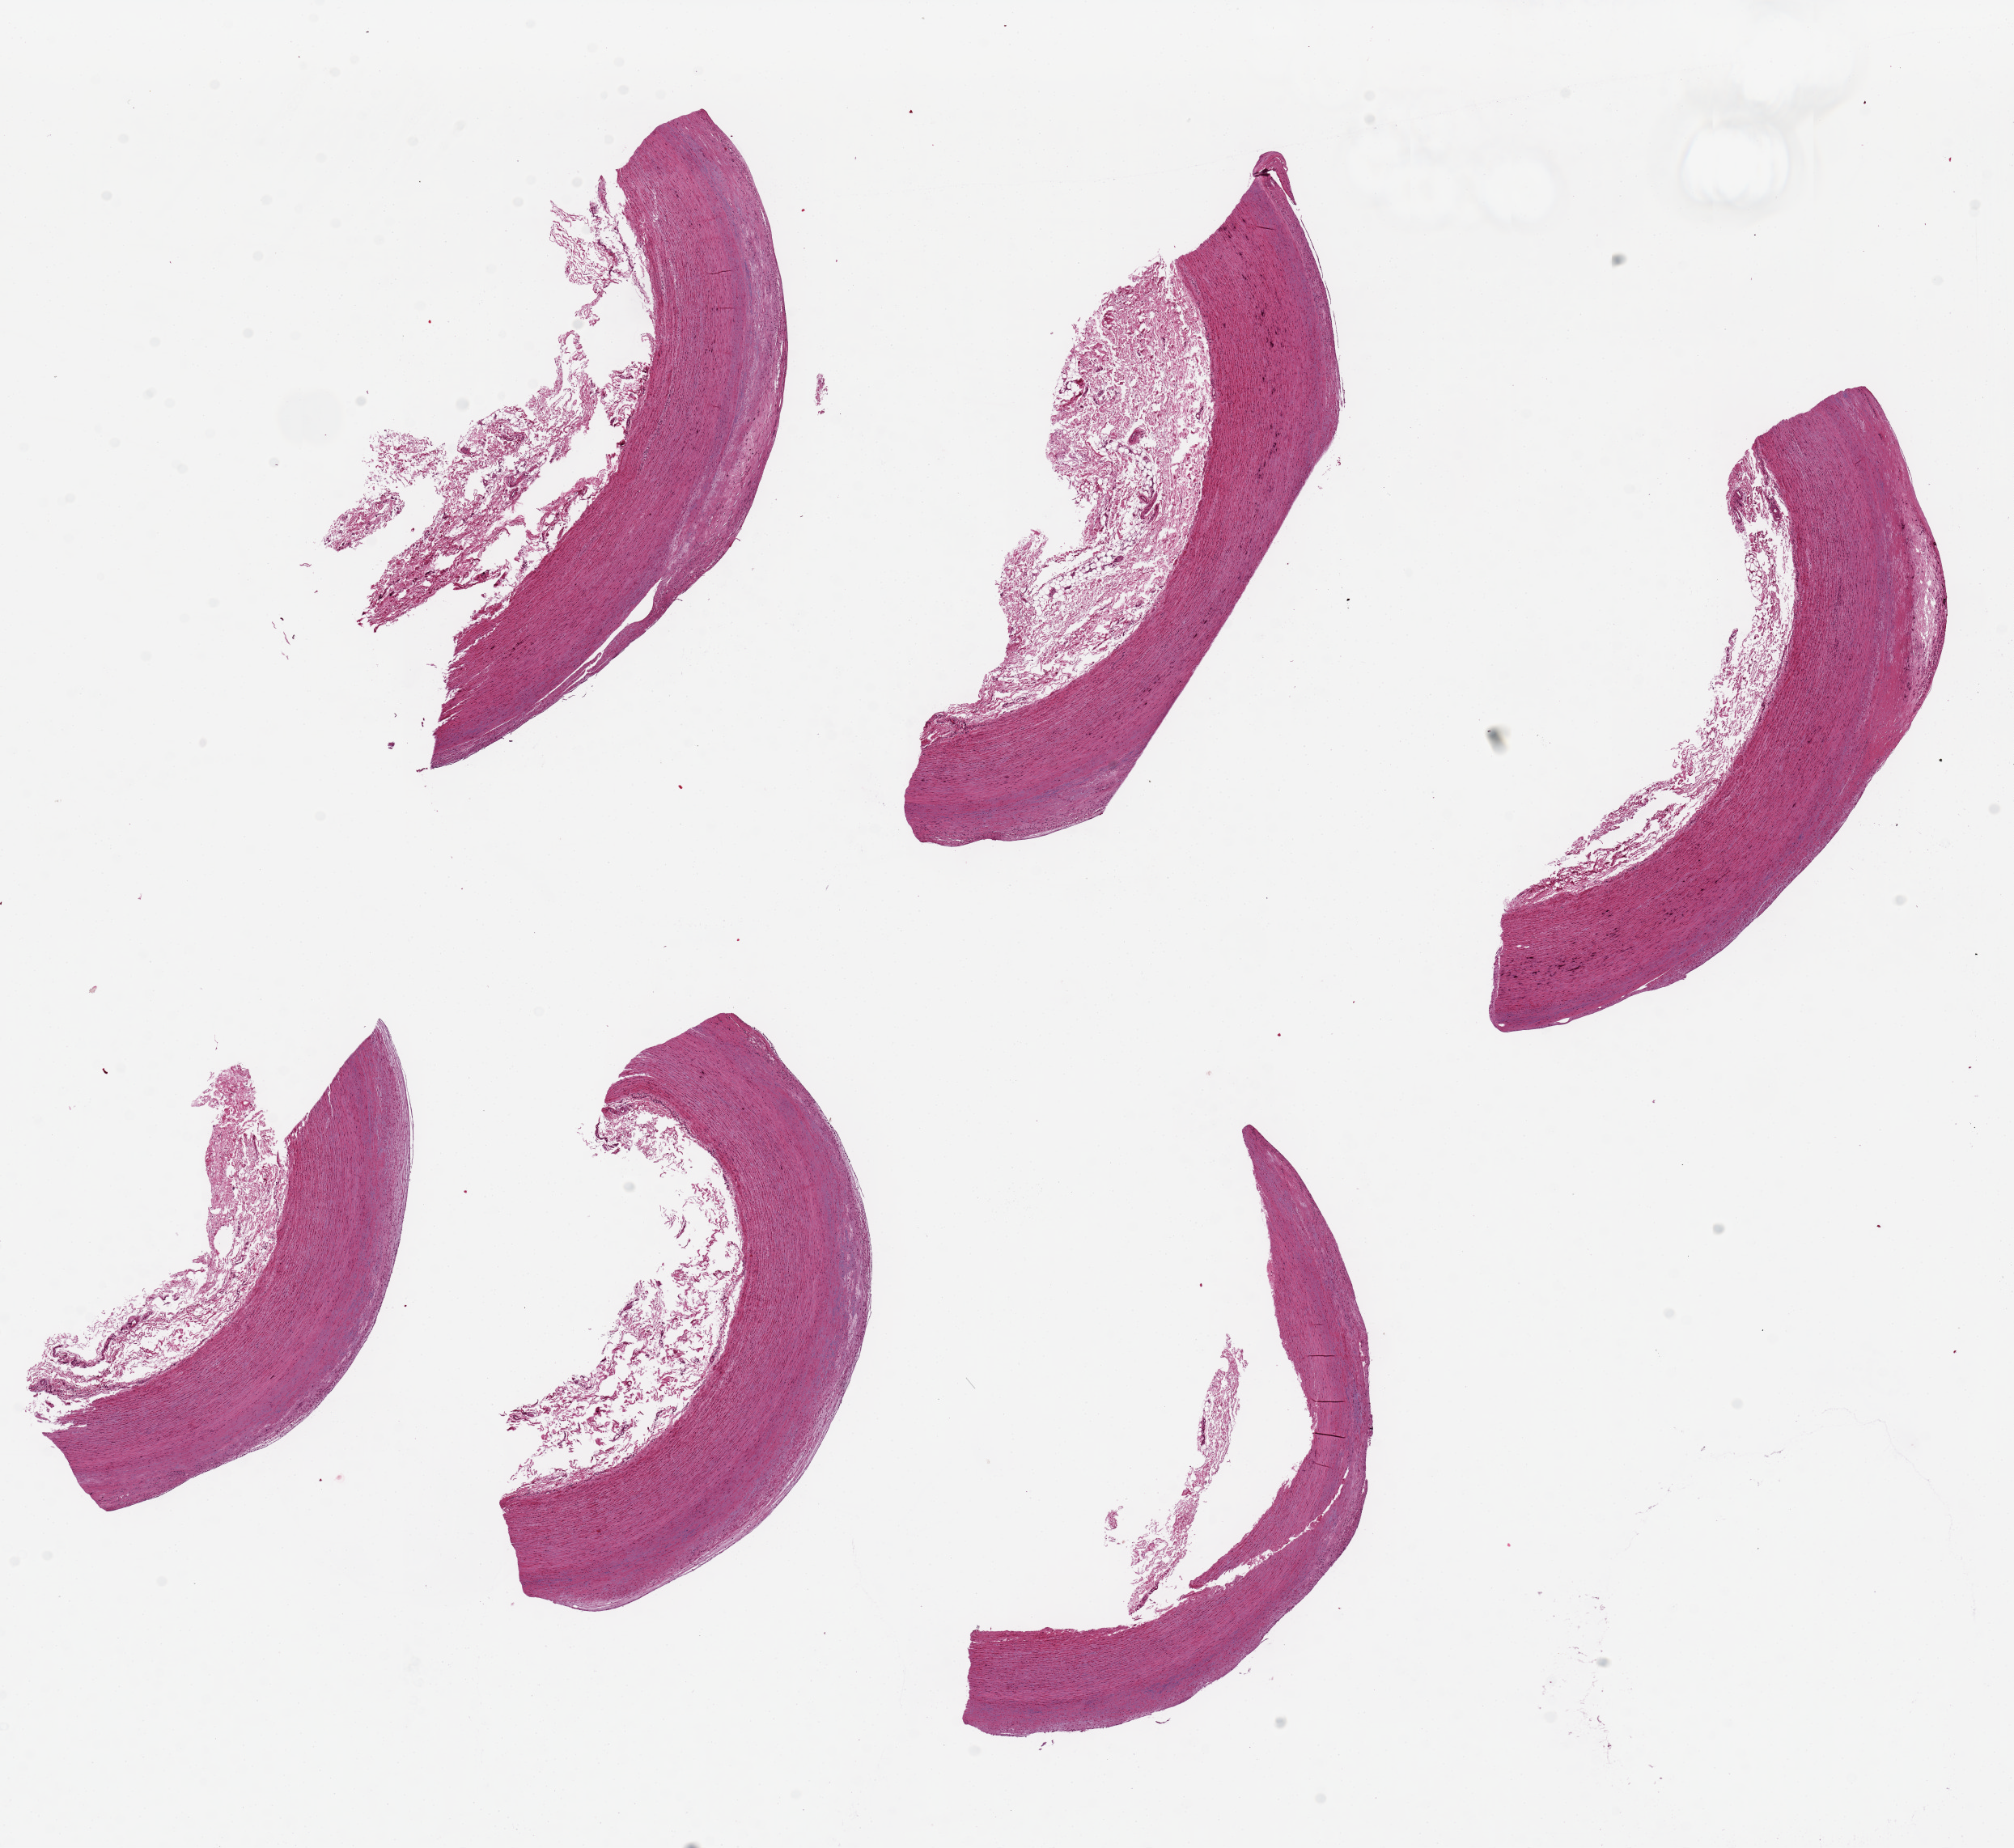
Digitized H&E-stained section — whole scanned area (about 19.7 x 18.1 mm, from a 20x scan) shown as a low-resolution overview; PAXgene-fixed, paraffin-embedded tissue; target tissue: aorta; tissue donor sample.
Pathologist's review note for this sample: 6 pieces, several with up to 1.5 mm adherent fibrous tissue.